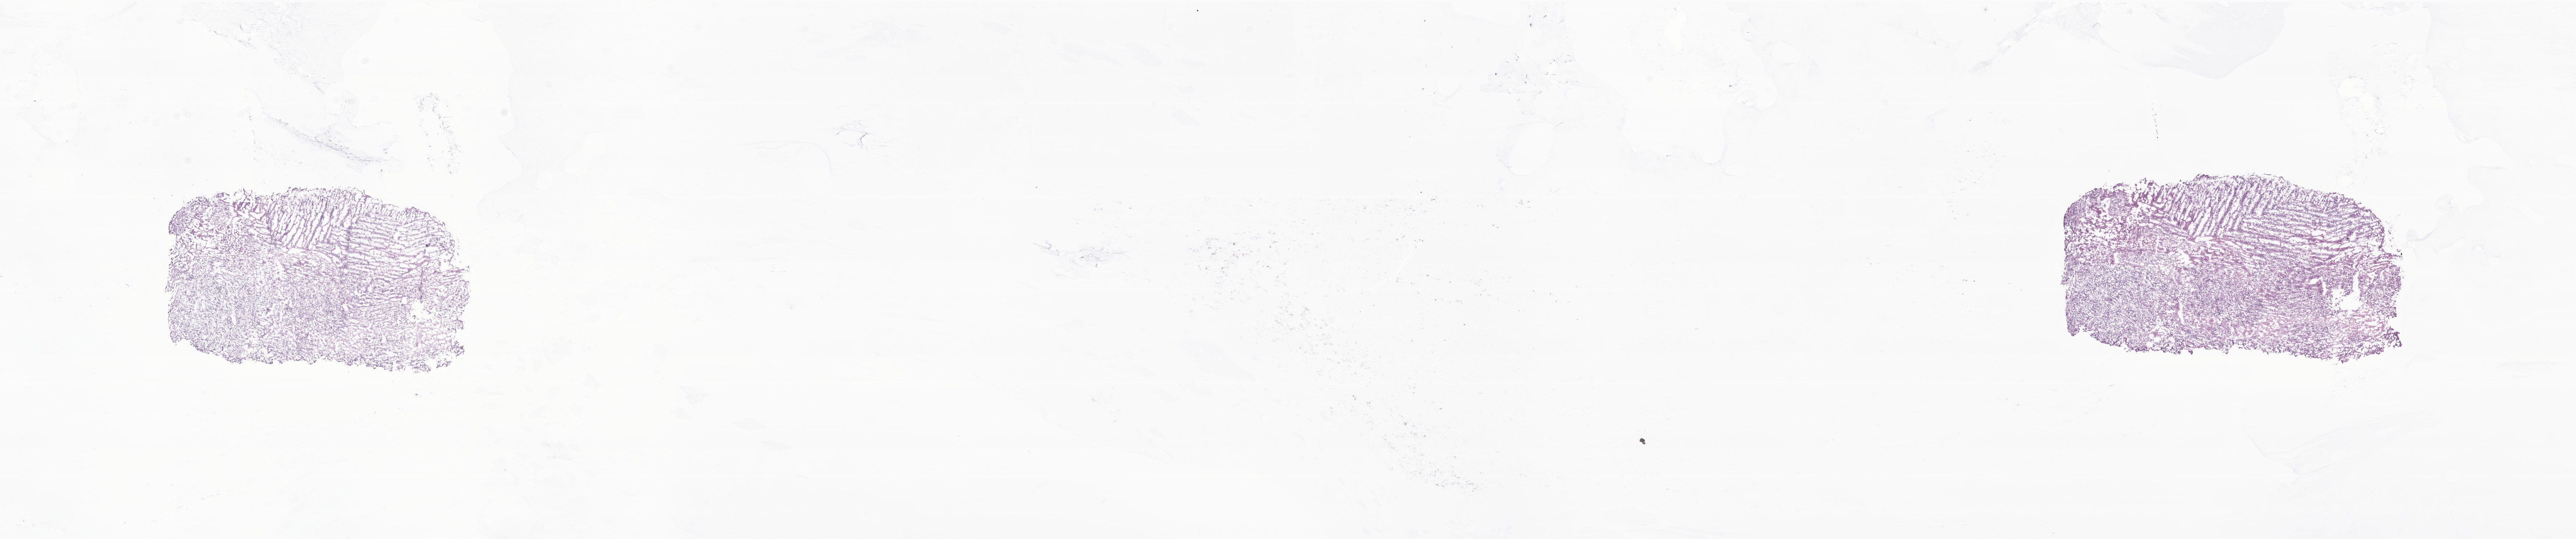
H&E whole-slide image of tumor tissue from the brain — shown as a low-resolution overview of the whole scanned area (about 29.5 x 6.2 mm), frozen section. Patient male; age 74 months (6 years 2 months).
Diagnosis: Ependymoma, NOS.